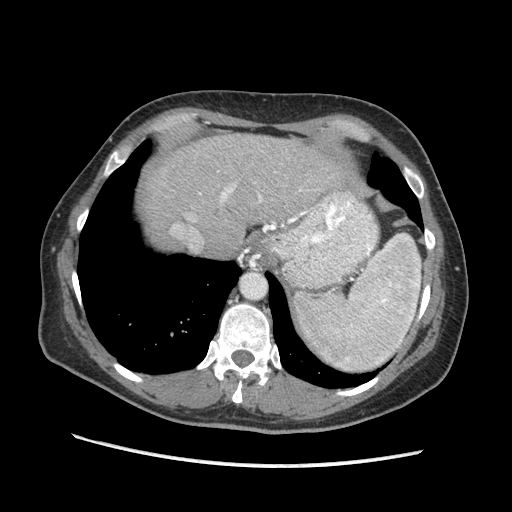
Contrast-enhanced abdominal CT (liver protocol), one axial slice; position 150 of 170 along the scan axis; reconstruction kernel STANDARD; 140 kVp; soft-tissue window (W 400 / L 40 HU); 2.5 mm slice thickness; 512 × 512 image matrix, field of view 360 × 360 mm. Case-level facts recorded for this patient, not image findings: diagnosis: hepatocellular carcinoma (patient treated with transarterial chemoembolisation; whether this scan precedes or follows treatment is not stated here); TNM stage (as recorded): Stage-II; Child-Pugh class: A; tumour differentiation: no biopsy.
Annotated regions visible in this slice (semi-automatically segmented with operator editing):
- abdominal aorta: box from (x=241, y=273) to (x=265, y=298) px
- liver parenchyma outside the tumour (the mass and vessels are separate outlines, so this box may not span the whole liver): (x=140, y=134)–(x=352, y=252)
- liver vessels: (x=177, y=188)–(x=296, y=227)